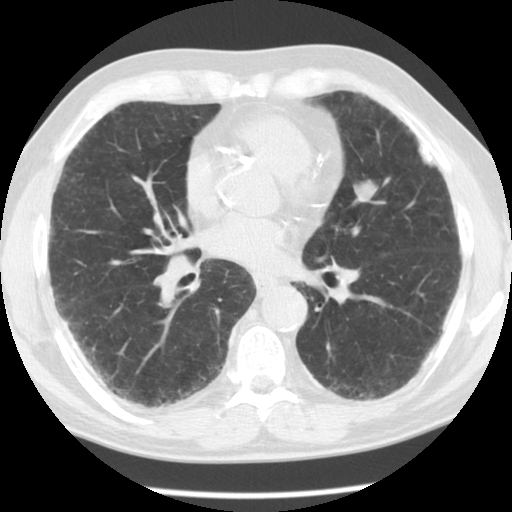
Low-dose screening chest CT, one axial slice. Slice 54 of 113 in the series (ordered by position). Reconstruction kernel STANDARD. Lung window (W 1500 / L -600 HU). 2.5 mm slice thickness. 512 × 512 image matrix, field of view 330 × 330 mm.
Outlined on this slice (outlined manually by an expert reader):
- lesion 1 (nodule, upper lobe of left lung): box from (x=353, y=180) to (x=378, y=201) px